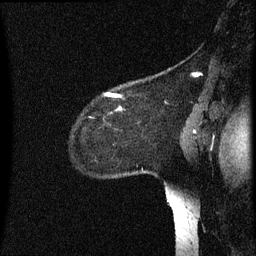
Breast MRI (dynamic contrast-enhanced), one sagittal slice. Position 51 of 60 along the scan axis. Dynamic contrast-enhanced series, image 2 of 3 at this slice position (ordered by acquisition). 1.5 T. TE 4.2 ms, TR 8.4 ms. 256 × 256 image matrix, field of view 200 × 200 mm. Female patient, age 35 years. Case-level facts recorded for this patient, not image findings: setting: breast cancer imaged before/during neoadjuvant chemotherapy; receptor status: HER2-positive.
Annotated regions visible in this slice (semi-automatic segmentation, software-assisted and operator-edited):
- analysis volume of interest (the breast-tissue region the enhancement analysis was run in; not a lesion): box from (x=82, y=78) to (x=155, y=173) px
- tumour enhancement mask (voxels above the 70 % enhancement threshold inside the analysis volume of interest): (x=107, y=94)–(x=119, y=97)